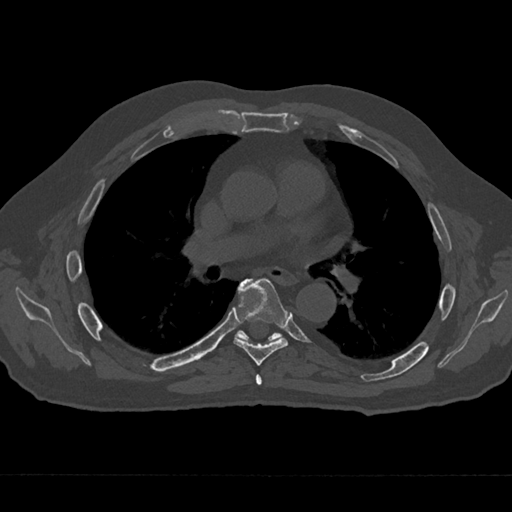
CT including the spine, one axial slice; position 408 of 797 along the scan axis; reconstruction kernel Br40s/3; 120 kVp; bone window (W 1800 / L 400 HU); 0.5 mm slice thickness; 512 × 512 image matrix, field of view 377 × 377 mm. Patient: male, 75 years. Case-level facts recorded for this patient, not image findings: primary cancer: renal.
Outlined on this slice (semi-automatically segmented with operator editing):
- T5 vertebra: bounding box <255,374,262,385> (left, top, right, bottom; pixels)
- T6 vertebra: <233,278,288,366>
- T7 vertebra: <236,281,280,342>